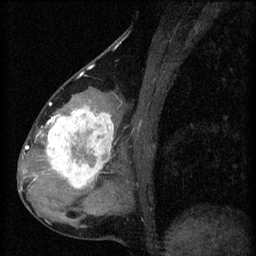
Breast MRI (dynamic contrast-enhanced), one sagittal slice; position 26 of 60 along the scan axis; 3 images stored at this slice position (order not interpretable as contrast timing); 1.5 T; TE 4.2 ms, TR 8.2 ms; 2 mm slice thickness; 256 × 256 image matrix, field of view 180 × 180 mm. Female patient, age 37 years.
Structures marked on this image (semi-automatic segmentation, software-assisted and operator-edited):
- analysis volume of interest (the breast-tissue region the enhancement analysis was run in; not a lesion): bounding box (x1, y1, x2, y2) in pixels: (44, 100, 119, 197)
- tumour enhancement mask (voxels above the 70 % enhancement threshold inside the analysis volume of interest): (44, 106, 115, 189)